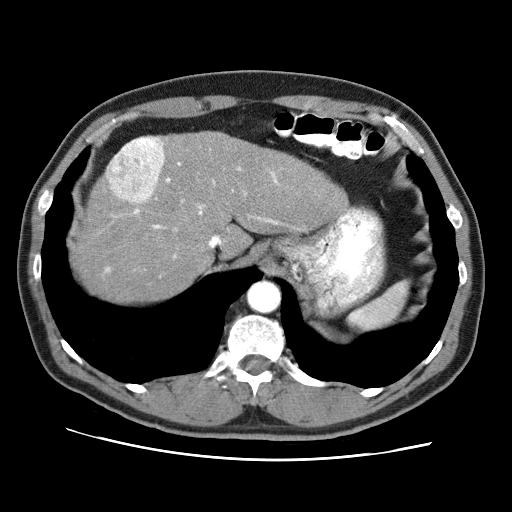
Contrast-enhanced abdominal CT (liver protocol), one axial slice; slice 56 of 71 in the series (ordered by position); soft-tissue window (W 400 / L 40 HU); 512 × 512 image matrix, field of view 360 × 360 mm. Case-level facts recorded for this patient, not image findings: diagnosis: hepatocellular carcinoma (patient treated with transarterial chemoembolisation; whether this scan precedes or follows treatment is not stated here); TNM stage (as recorded): Stage-II; Child-Pugh class: A; tumour nodularity: multinodular; tumour size: 4.6 cm.
Outlined on this slice (semi-automatic segmentation, software-assisted and operator-edited):
- abdominal aorta: bounding box (x1, y1, x2, y2) in pixels: (248, 282, 279, 311)
- liver parenchyma outside the tumour (the mass and vessels are separate outlines, so this box may not span the whole liver): (72, 132, 348, 302)
- mass: (104, 135, 165, 203)
- liver vessels: (106, 163, 277, 271)